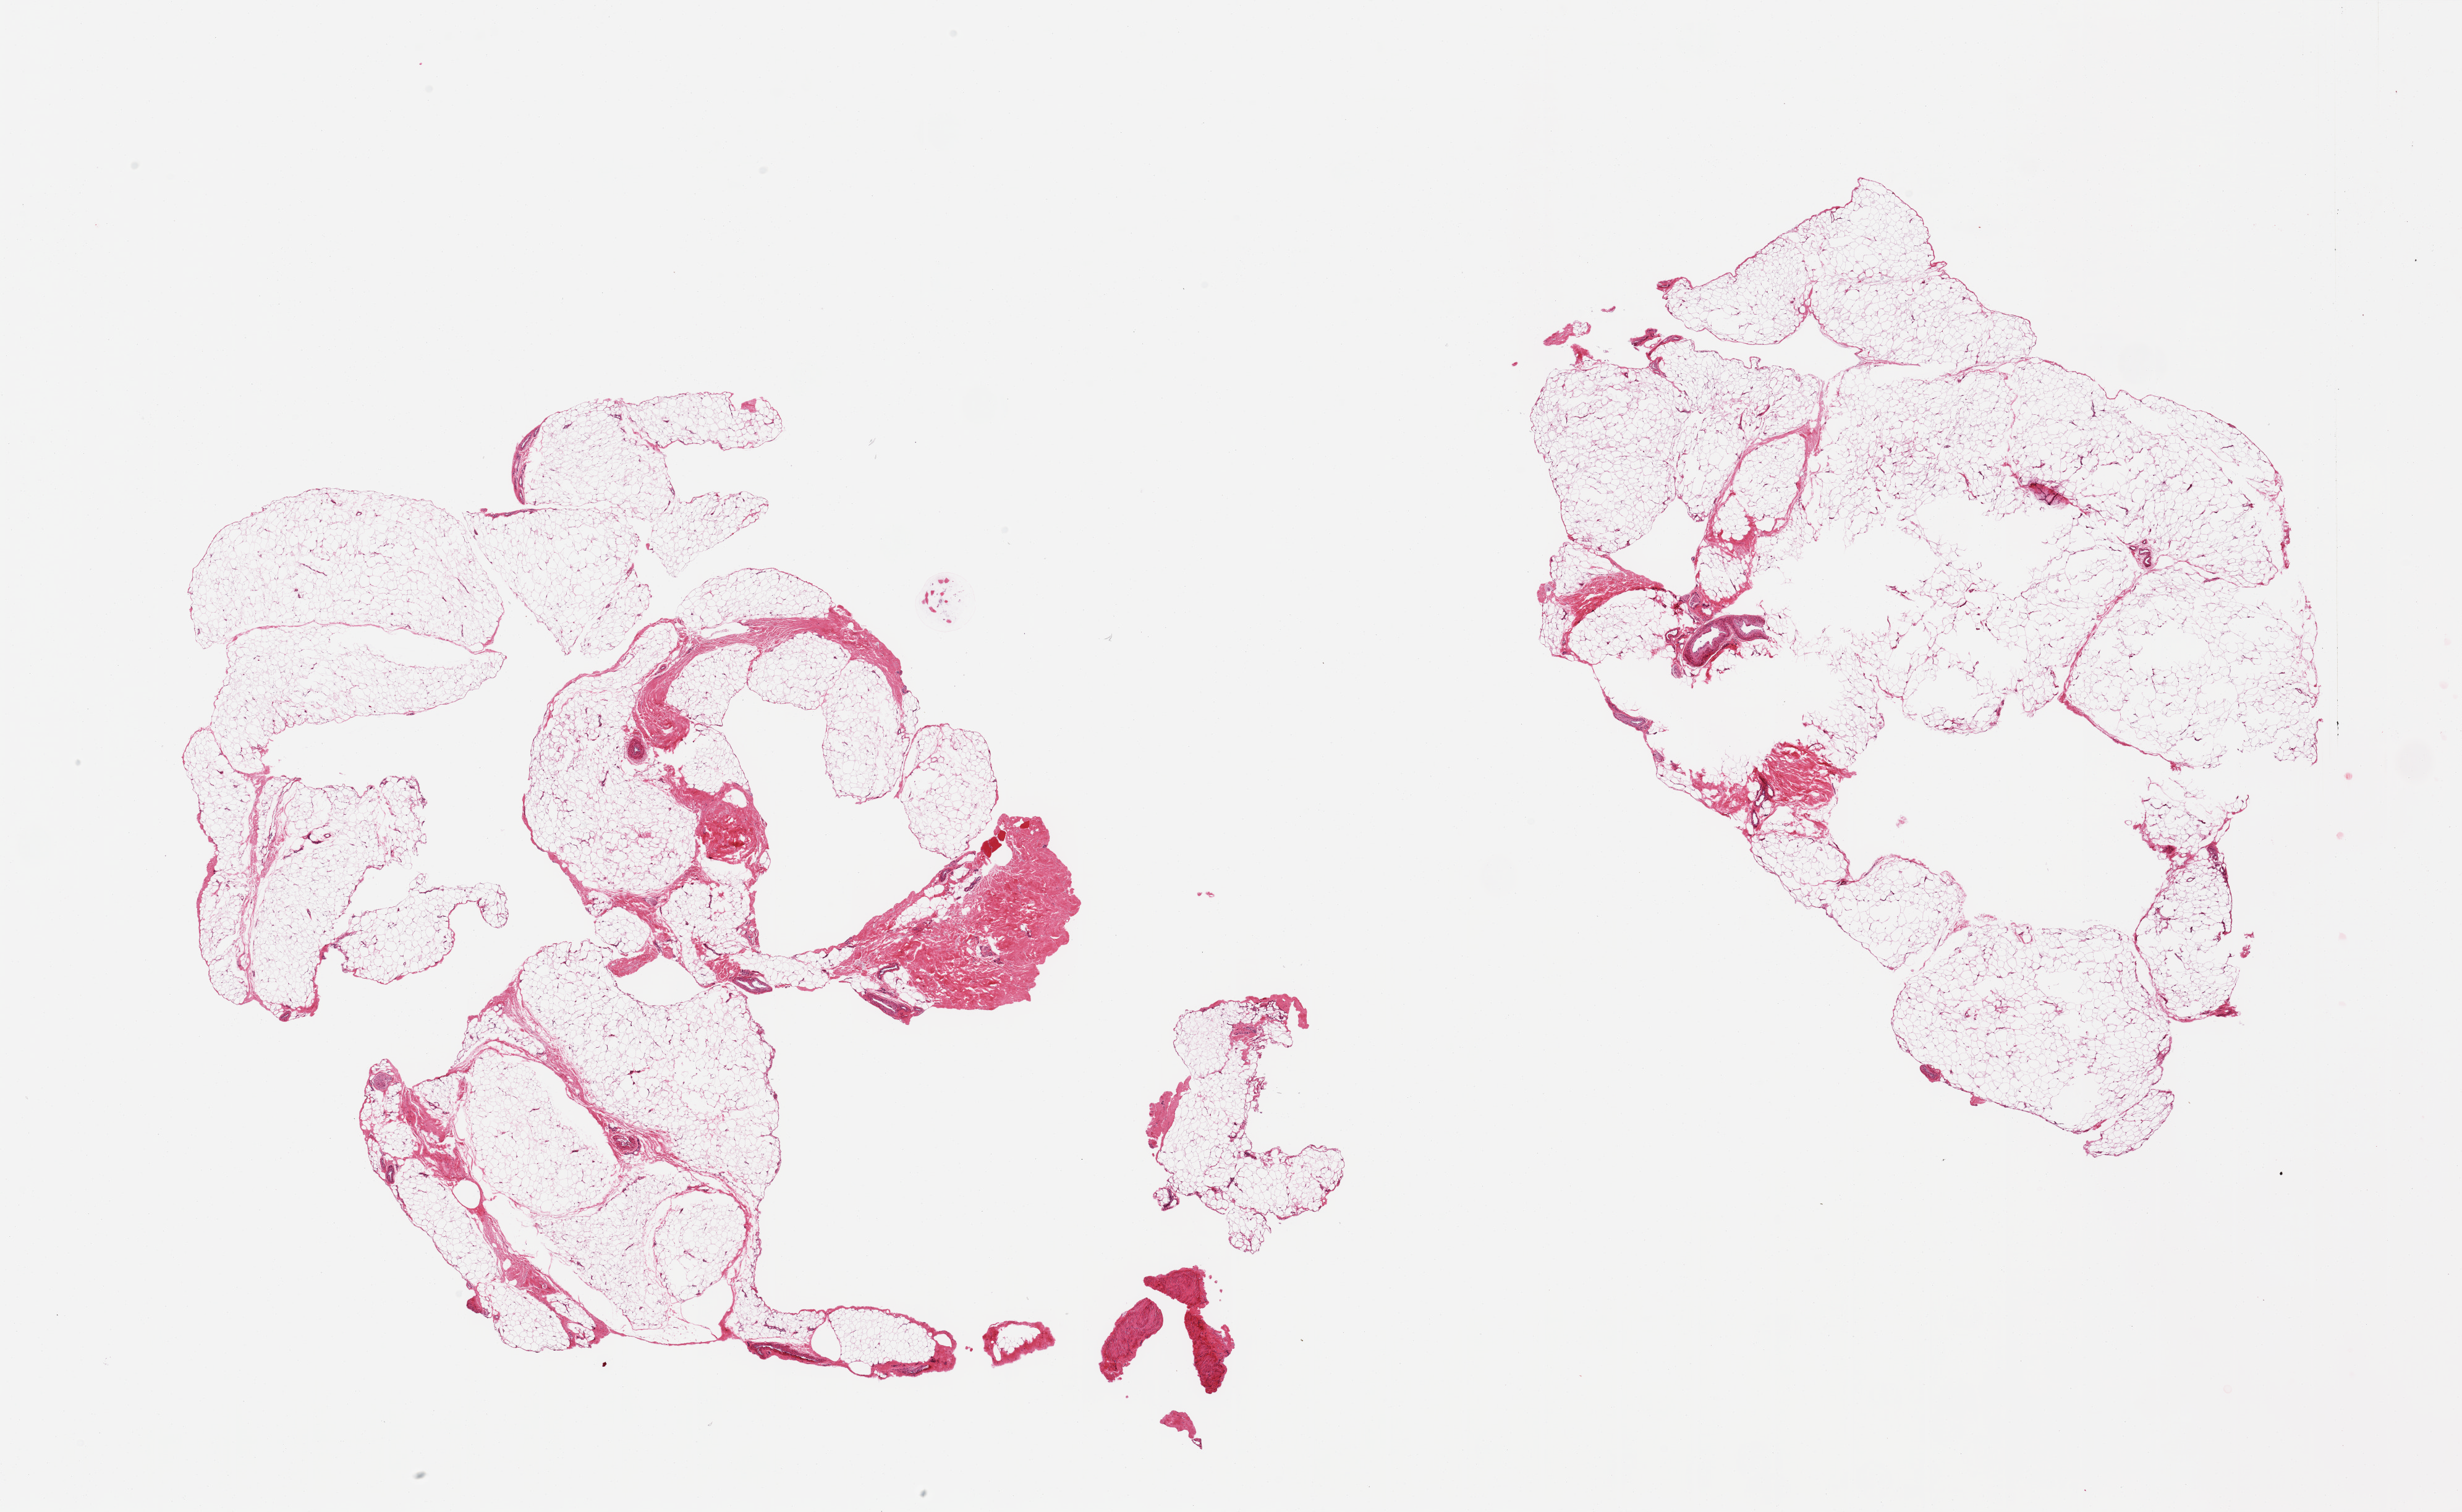
H&E whole-slide image — whole scanned area (about 31.5 x 19.3 mm) shown as a low-resolution overview; PAXgene-fixed paraffin-embedded (PFPE) section; sampled site (target tissue): adipose tissue; donor tissue sample. Donor: male.
Reviewer comment on this tissue sample: 2 pieces; mature adipose tissue and fibrovascular component.